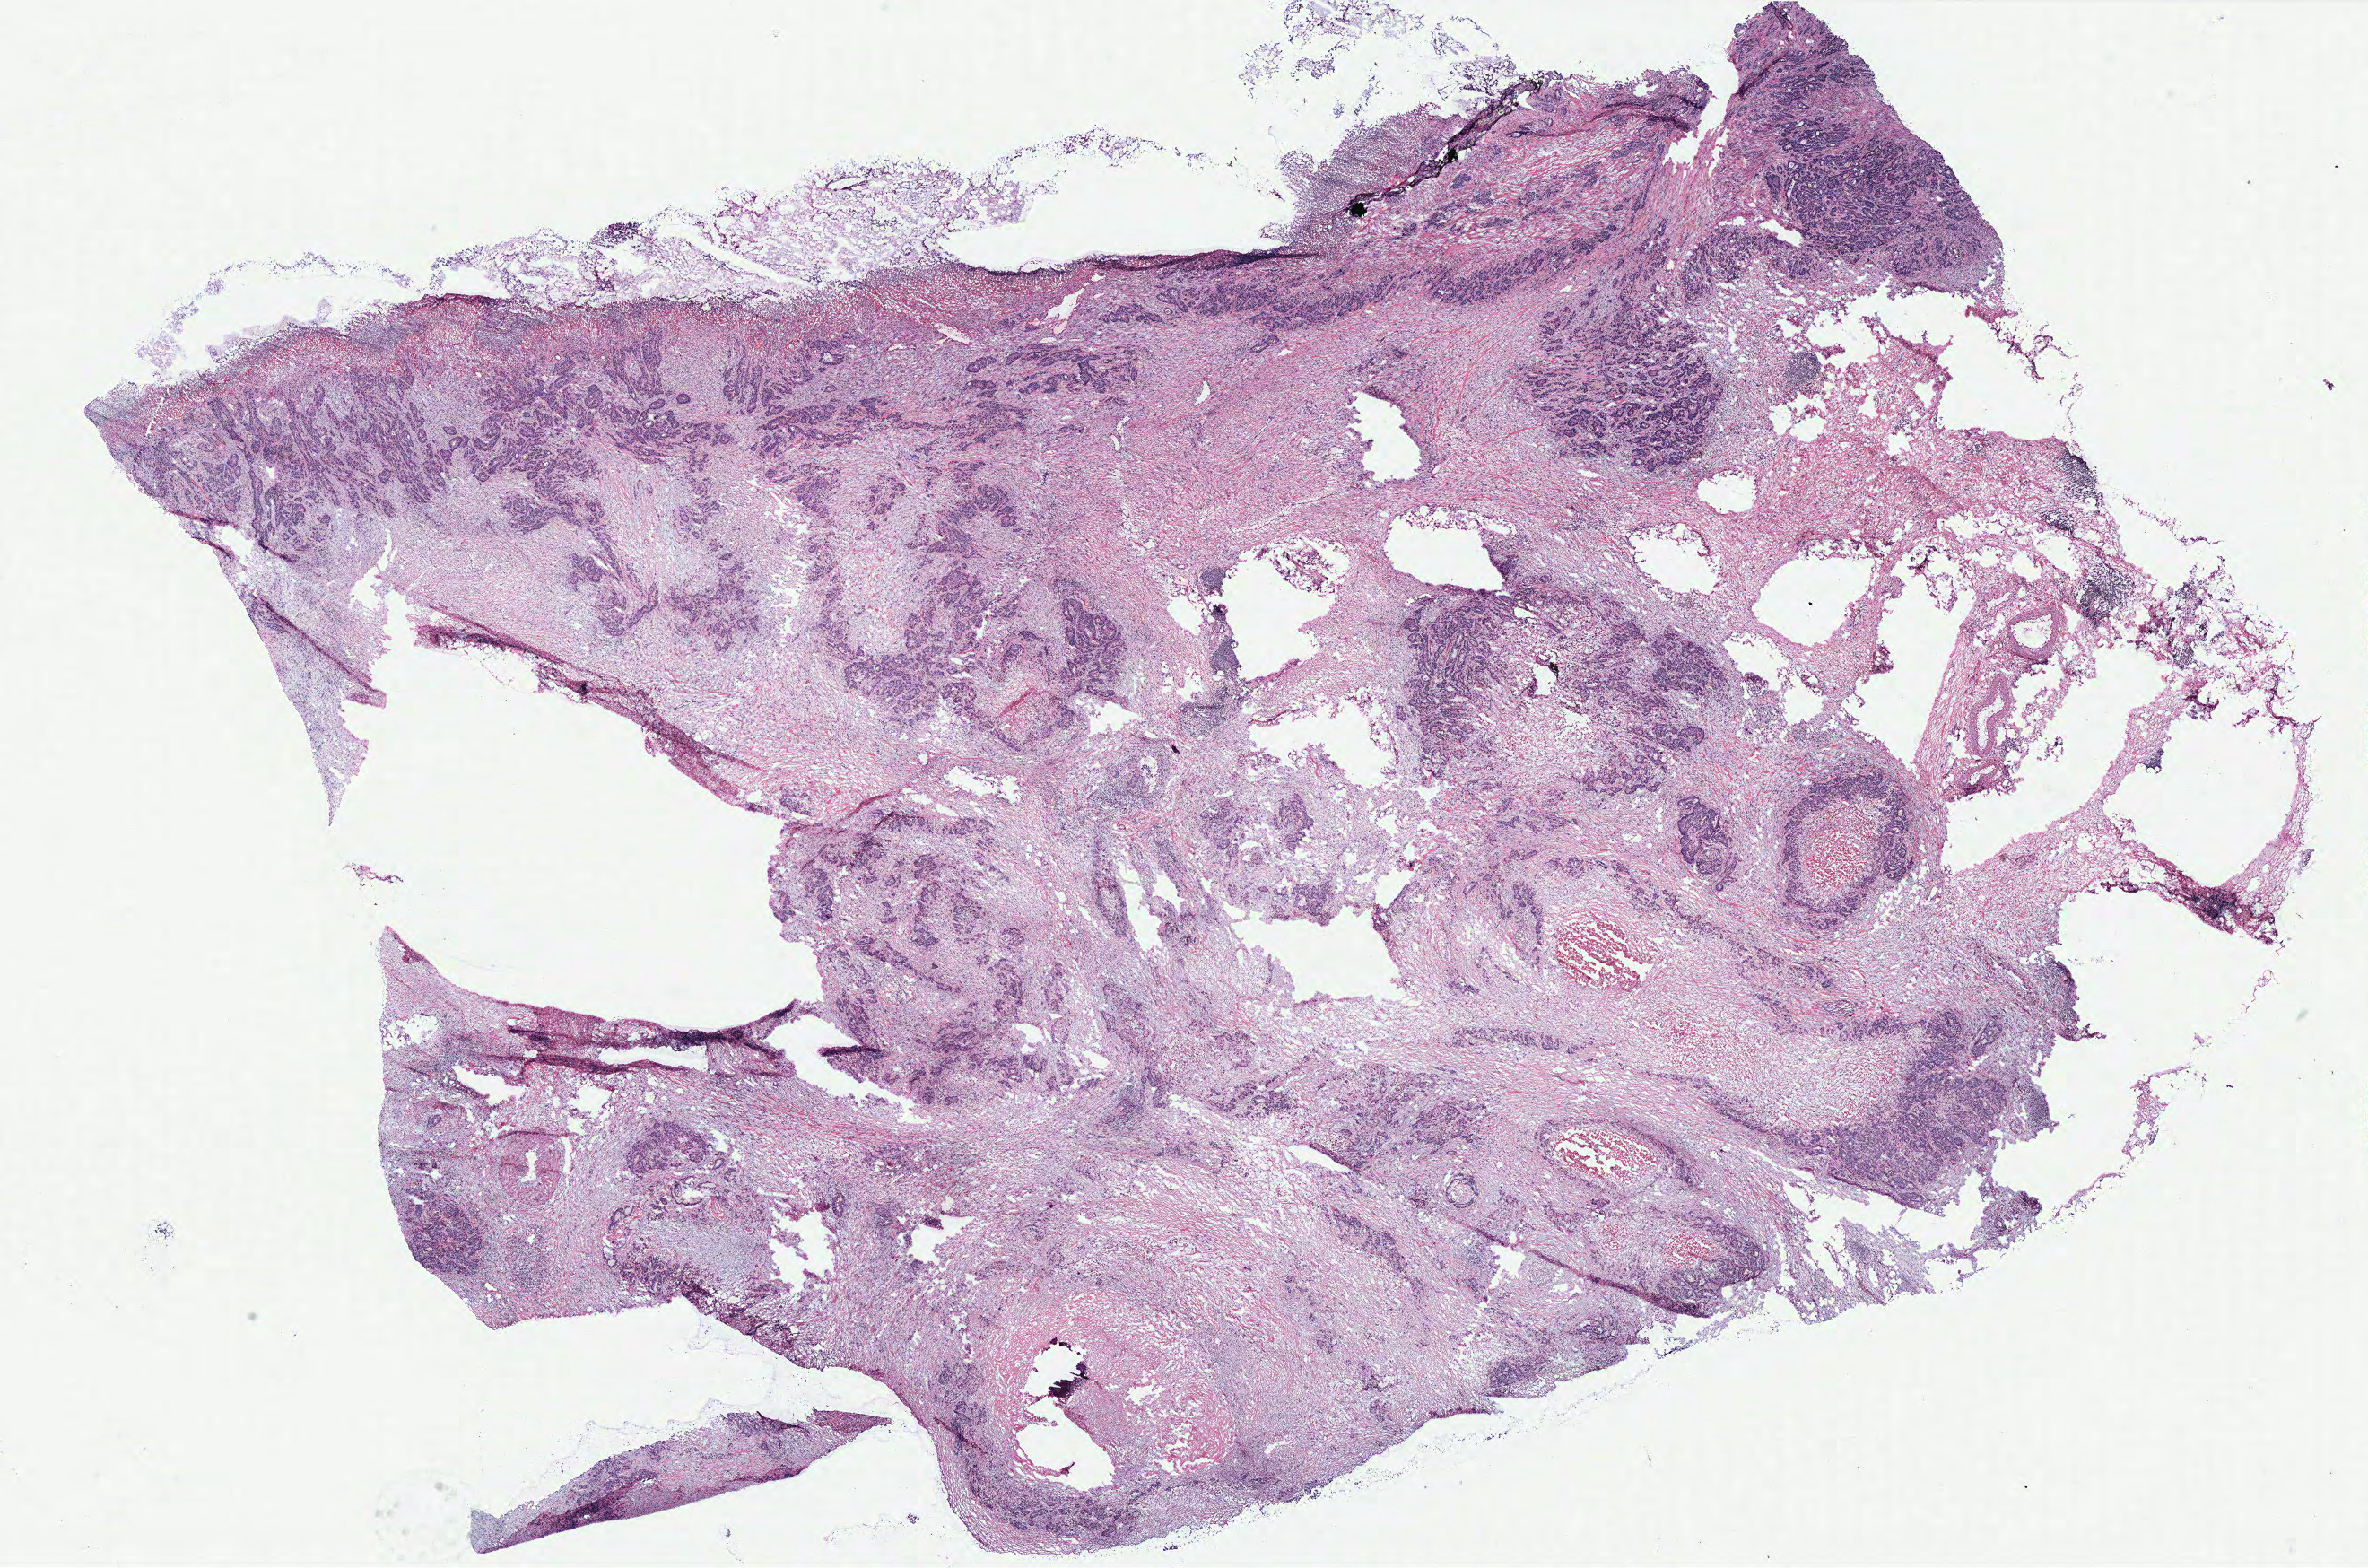
Digitized H&E tissue section (whole slide) — whole scanned area (about 21.1 x 14.0 mm, from a 40x scan) shown as a low-resolution overview. Colon, tissue type not recorded.
Patient diagnosis (cohort enrolment): colon cancer (colon).